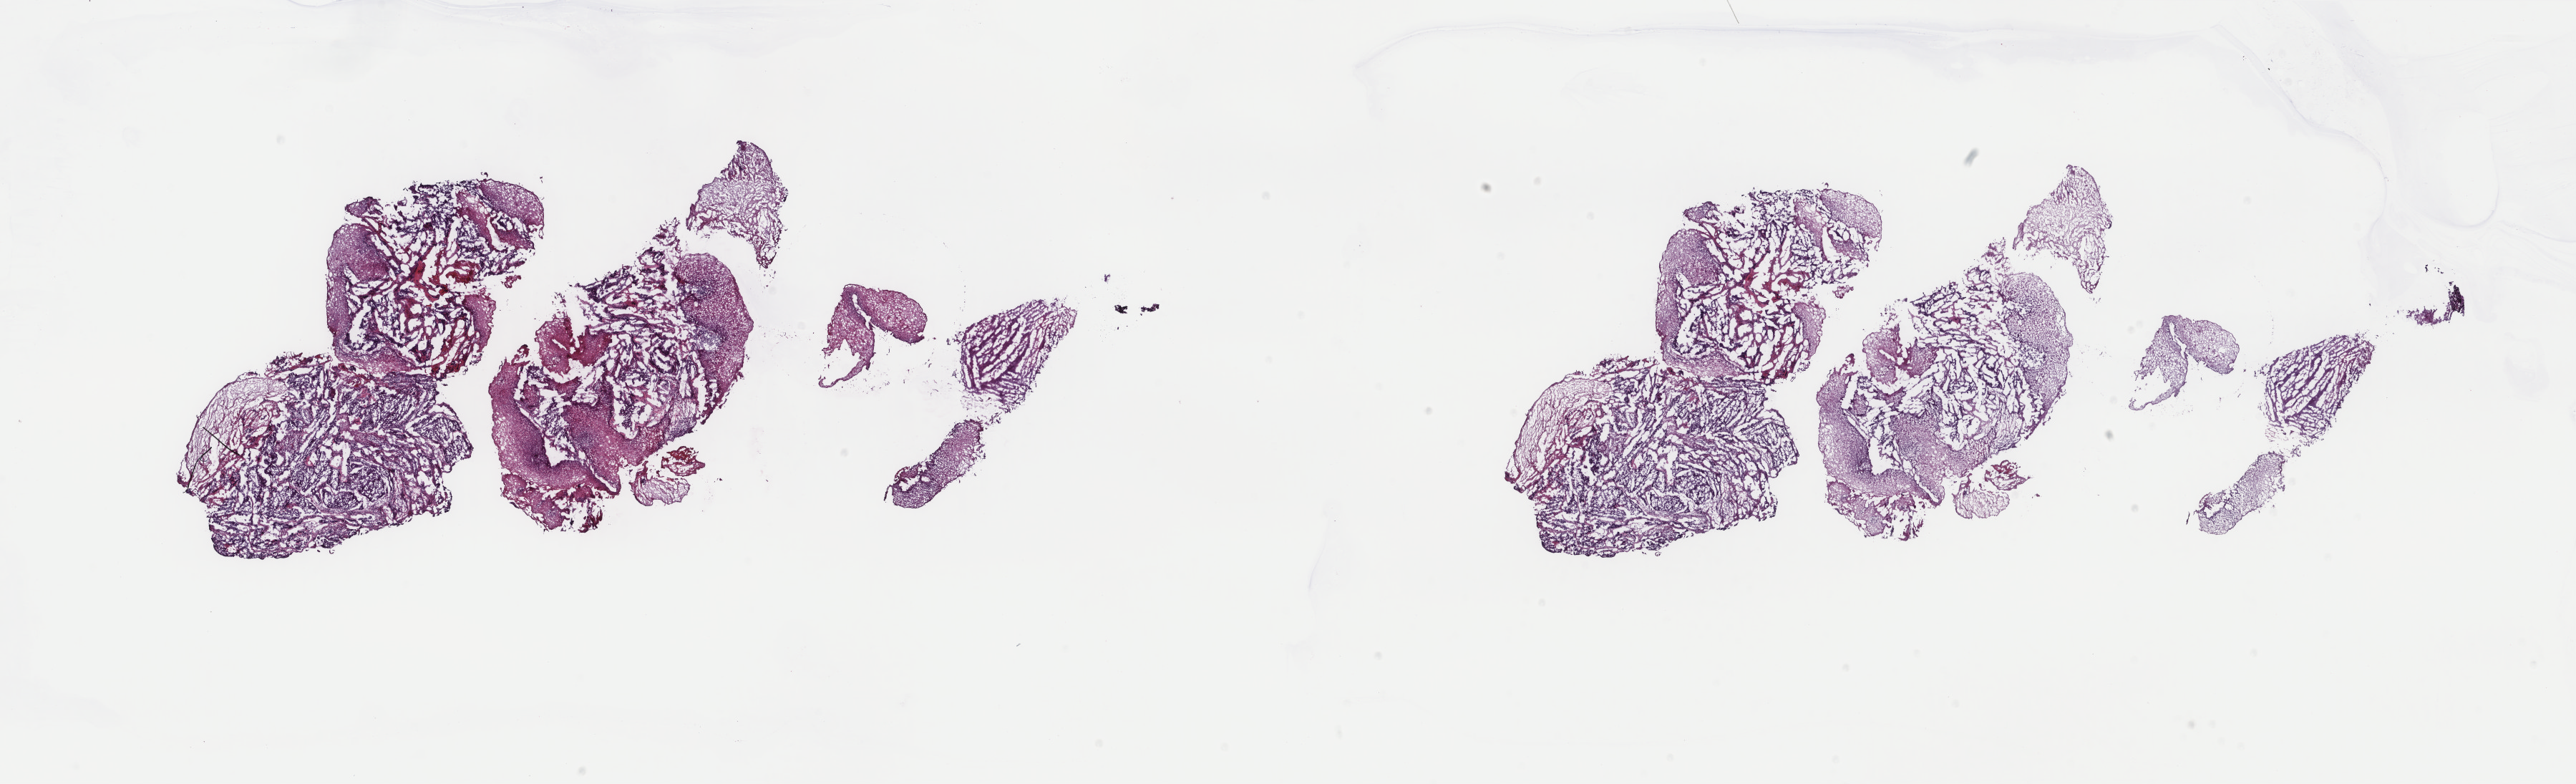
Whole-slide histology image, Hematoxylin and eosin (H&E) stained — shown as a low-resolution overview of the whole scanned area (about 28.6 x 8.7 mm), frozen section from the top of the tissue portion, primary tumour sample from the esophagus. Patient: male, age at initial diagnosis 65 years. Histologic grade: G3 (poorly differentiated). Composition of this section per pathologist review: tumour cells 50%, tumour nuclei 100%, normal cells 0%, stromal cells 45%, necrosis 5%. Inflammatory infiltration, as recorded: lymphocyte infiltration 1%, monocyte infiltration 2%, neutrophil infiltration 0%.
• diagnosis: Squamous cell carcinoma, NOS (lower third of esophagus)